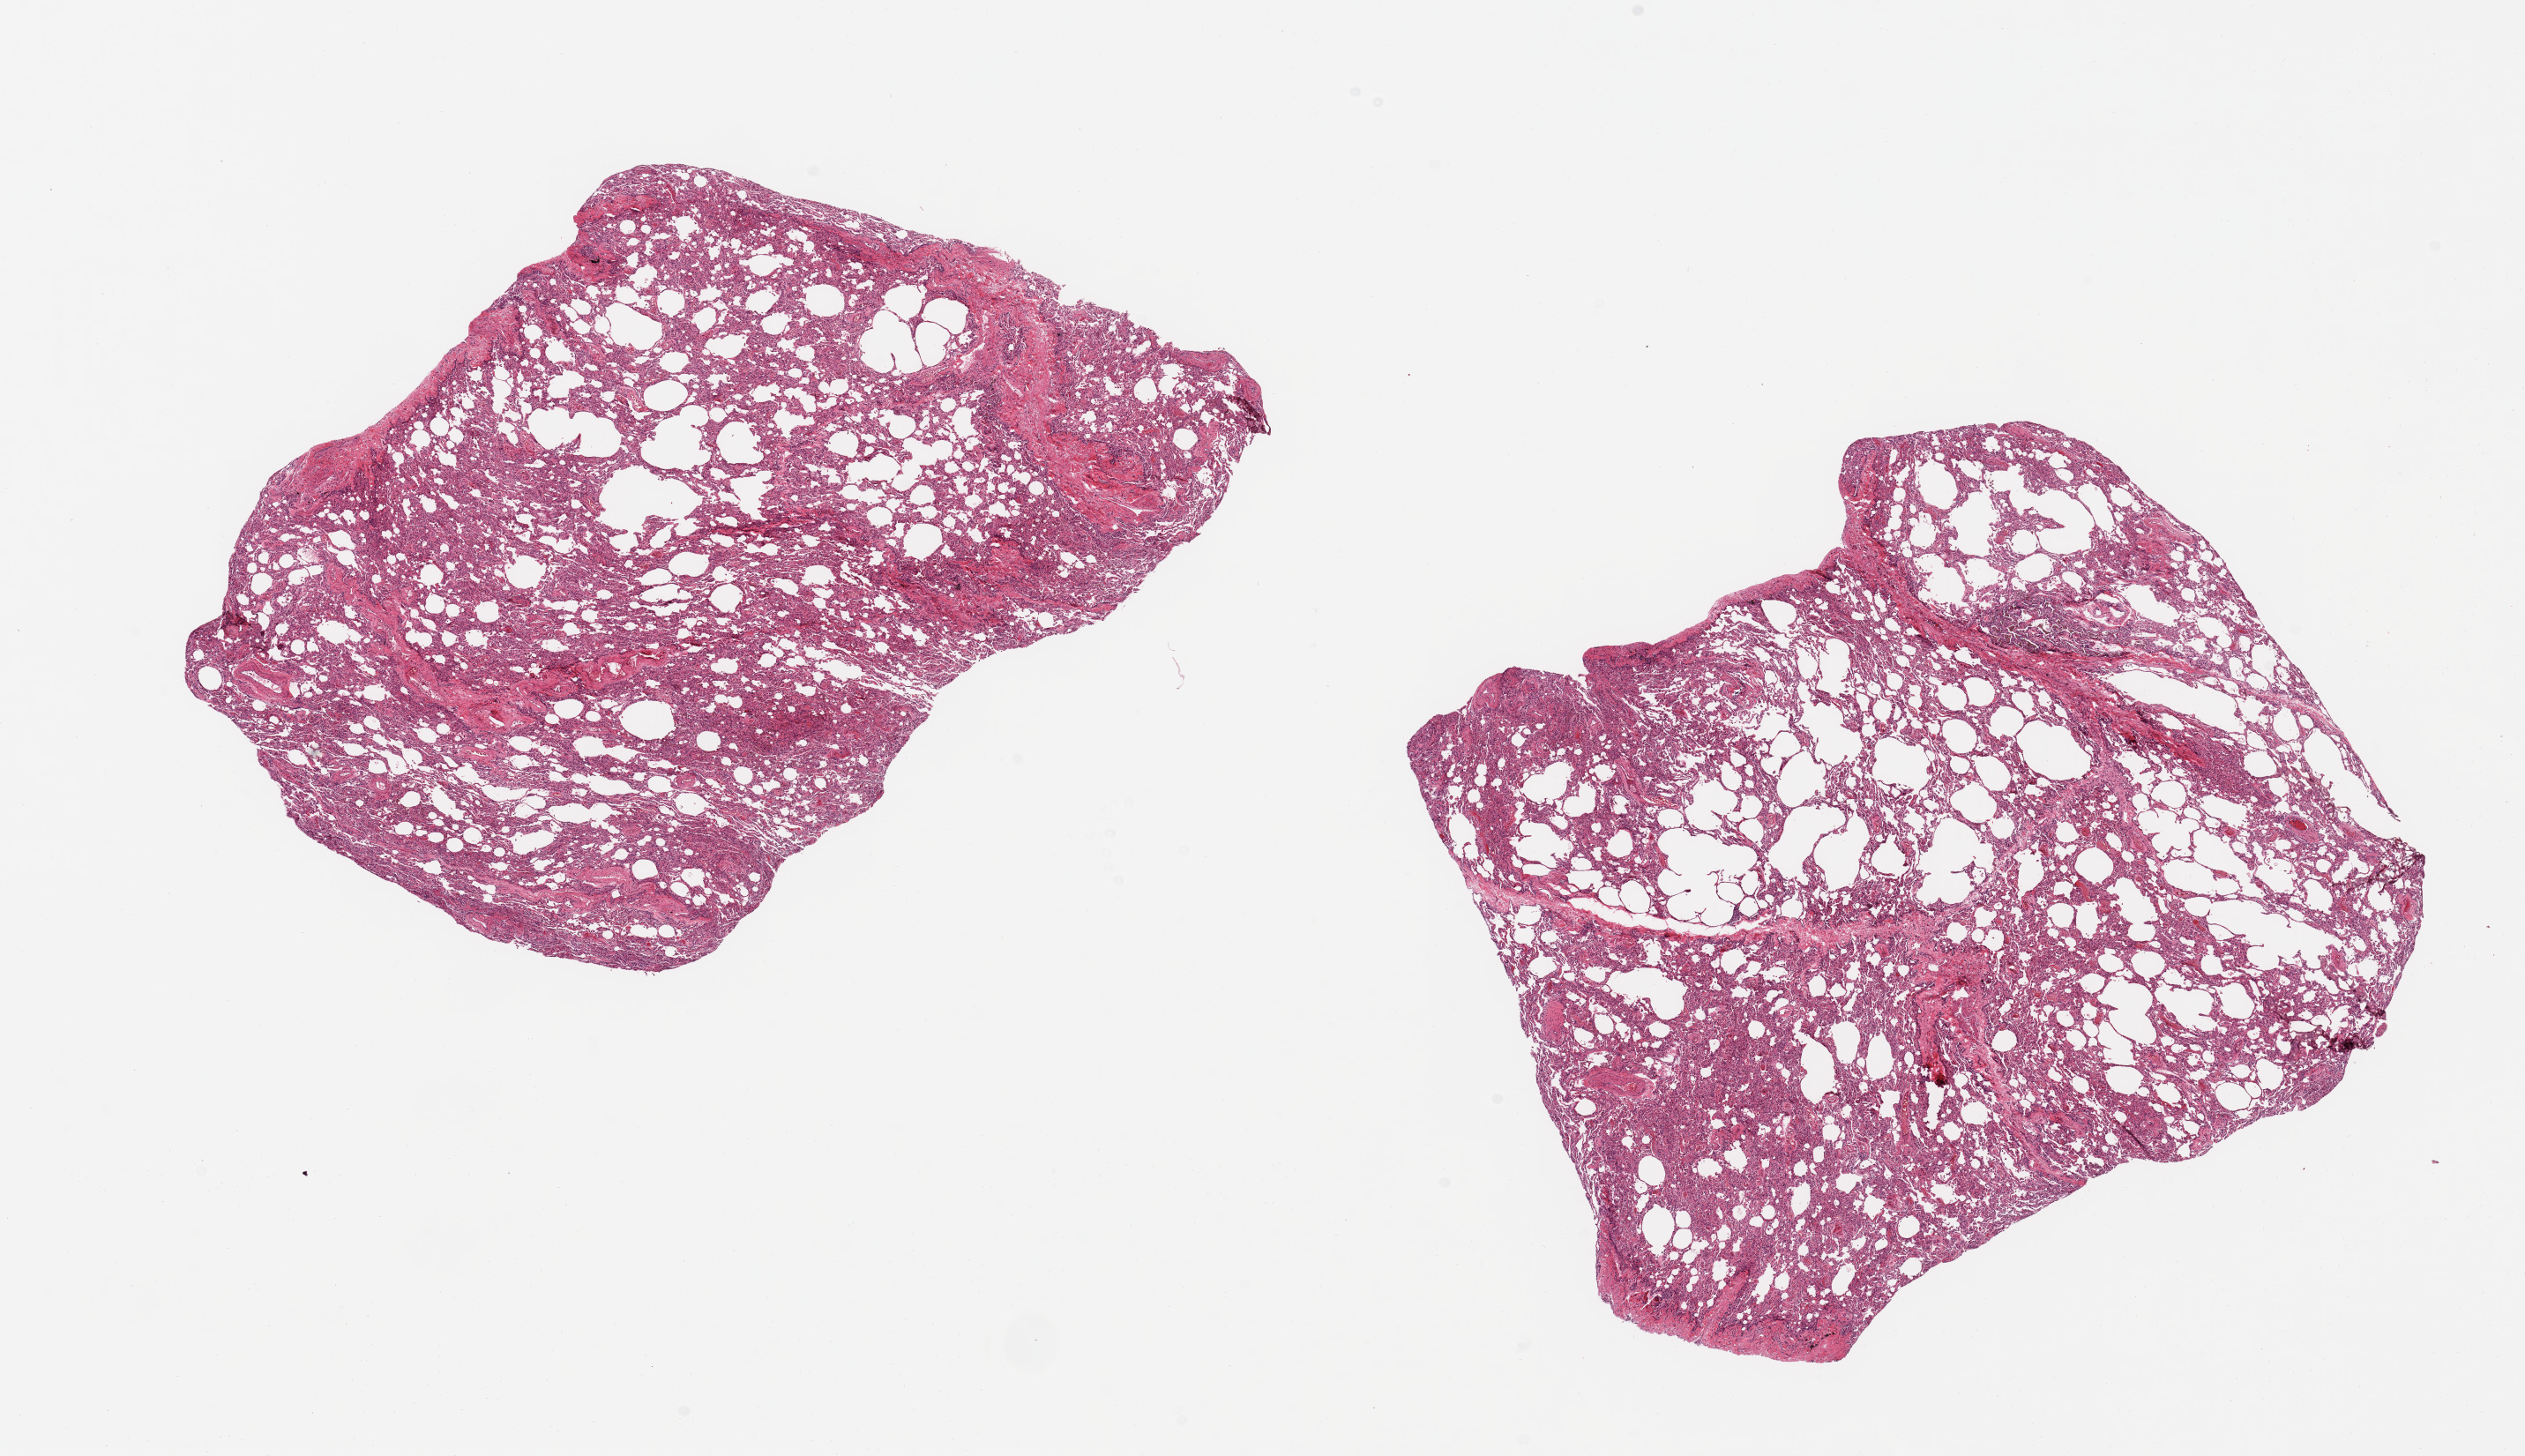
Whole-slide image, H&E stain, brightfield, whole scanned area (about 22.6 x 13.1 mm, slide scanned at 20x) shown as a low-resolution overview. PAXgene-fixed, paraffin-embedded tissue. Section of lung (target tissue). Tissue donor sample. Donor sex: male.
Review note (as recorded): 2 pieces; atelectasis alternating with dilated alveolar spaces (likely secondary to ventilator); congestion and hemosiderinophages.